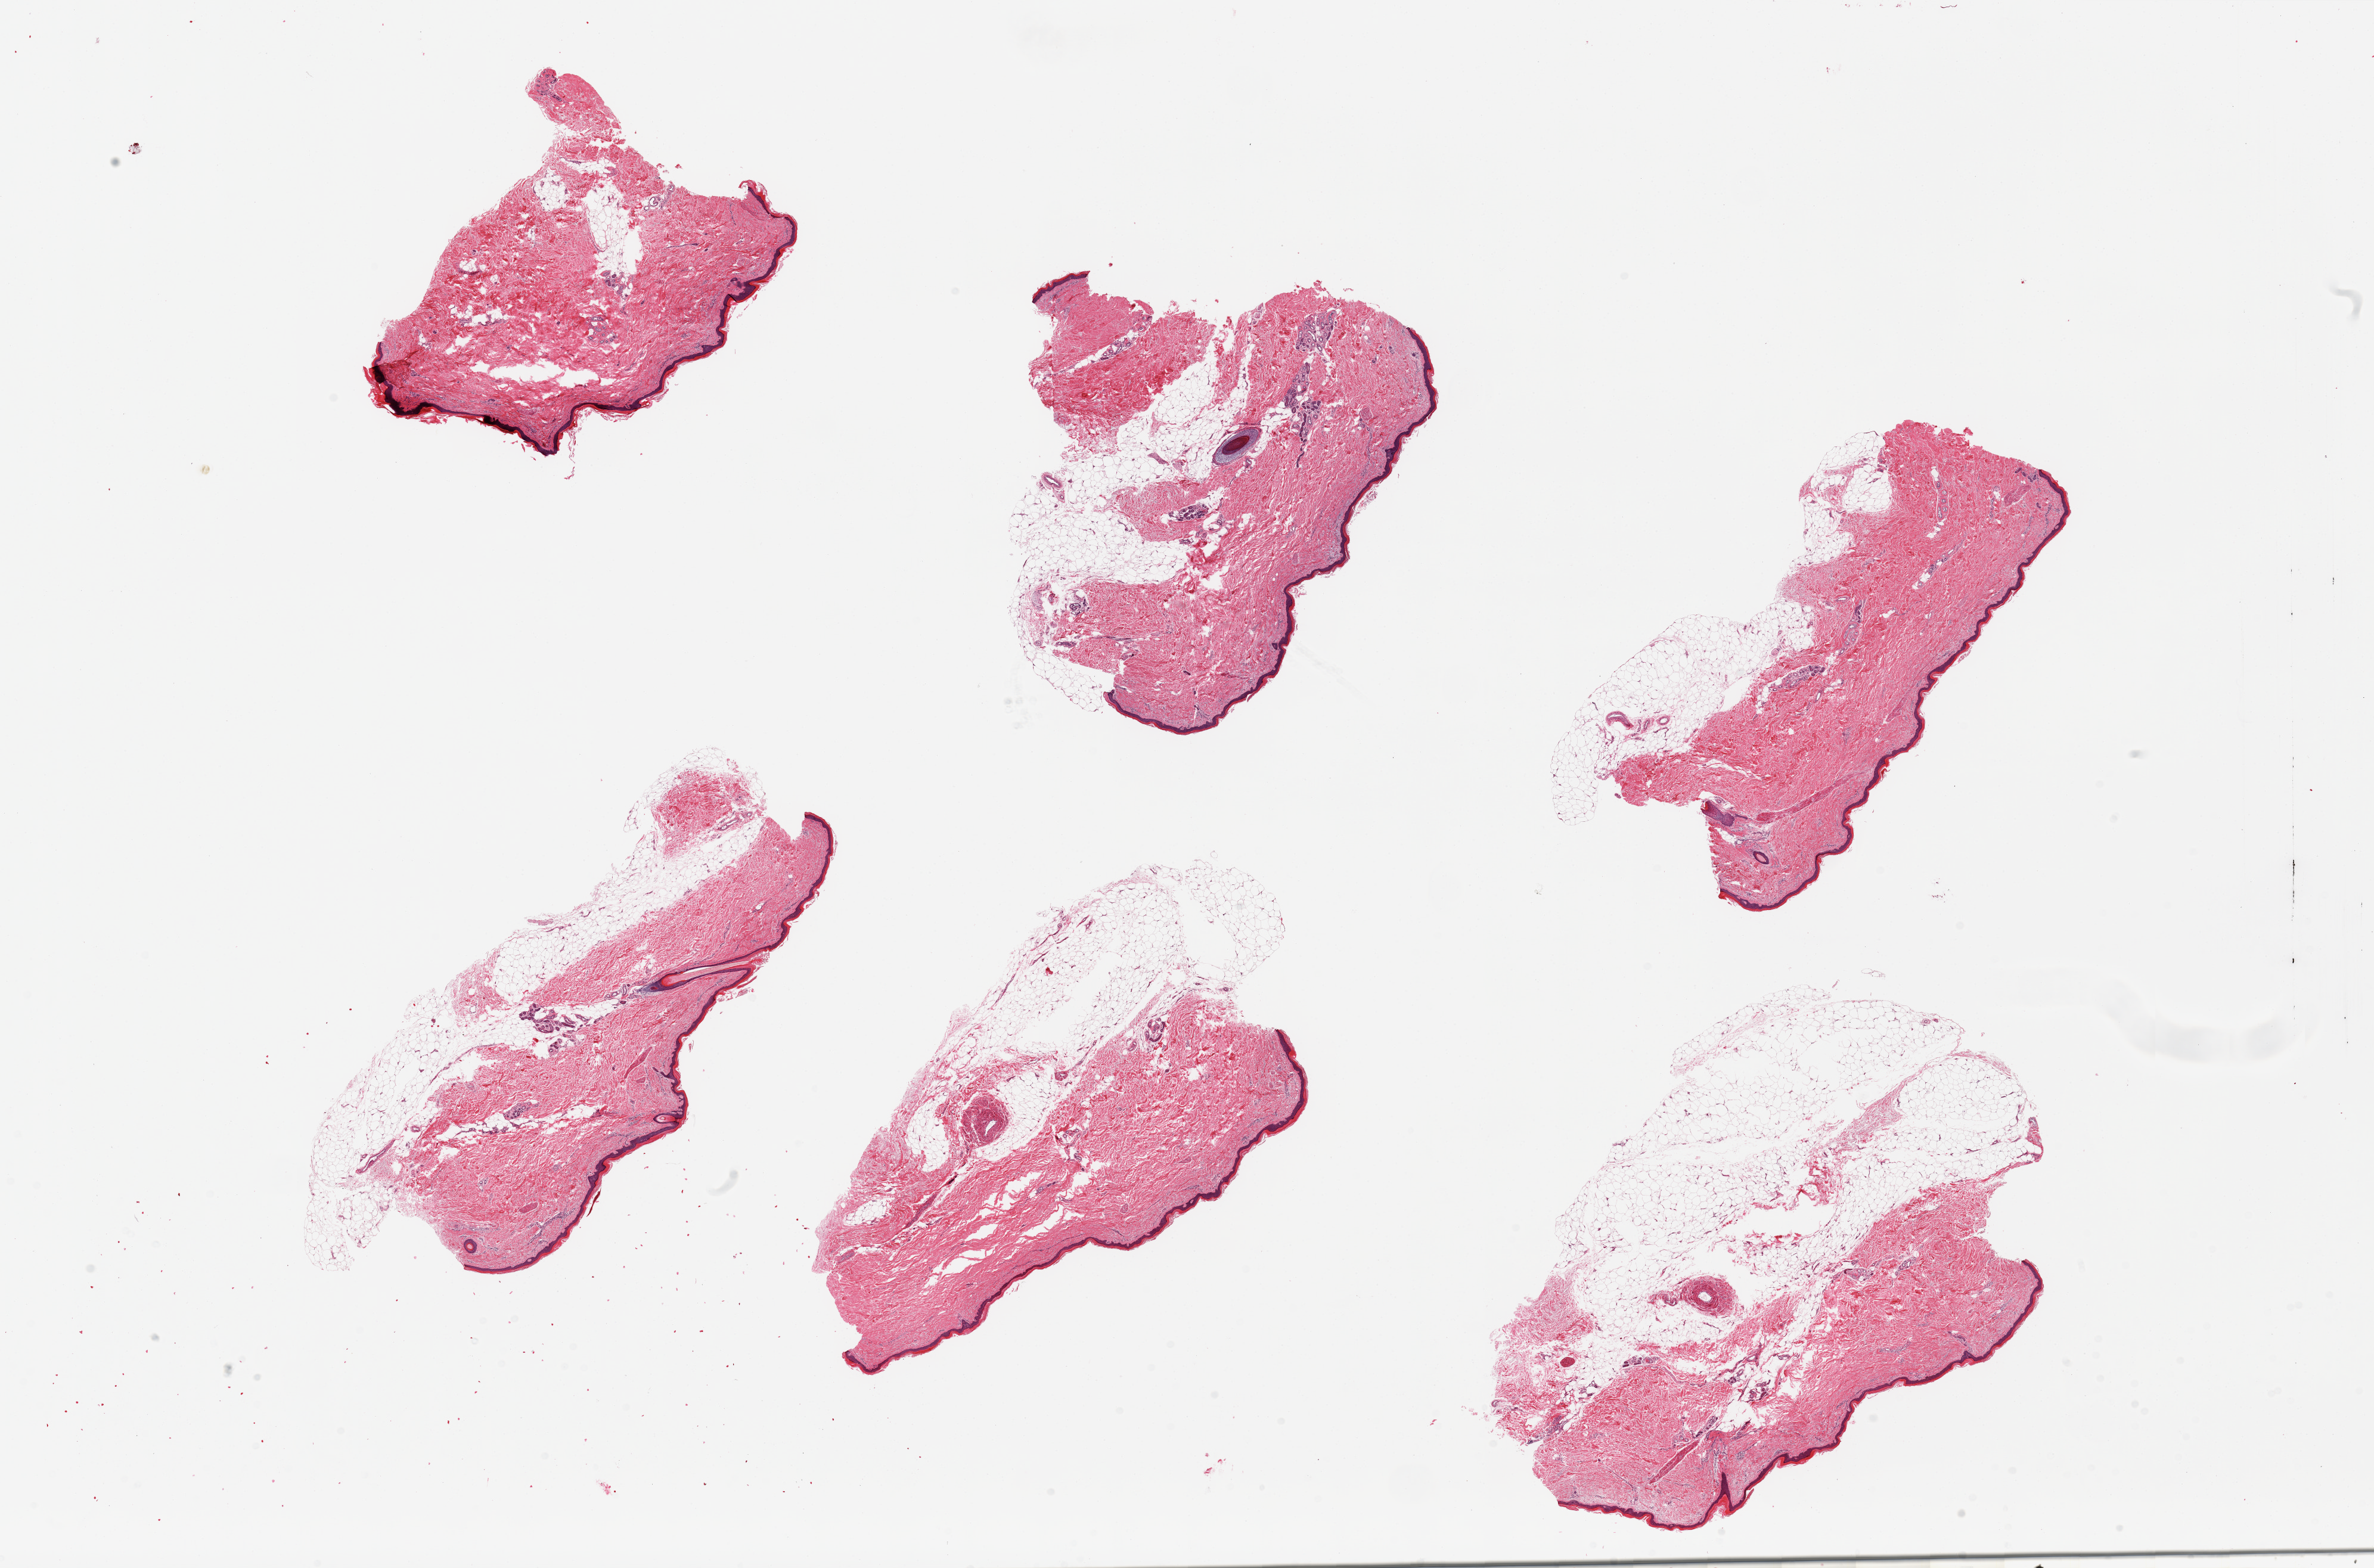
Haematoxylin and eosin whole-slide image — whole scanned area (about 31.5 x 20.8 mm, from a 20x scan) shown as a low-resolution overview; PAXgene-fixed paraffin-embedded (PFPE) section; target tissue: skin of lower leg; tissue donor sample. Donor: male.
Reviewer comment on this tissue sample: 6 pieces, adherent fat up to 3mm thick, squamous epithelium is ~50-60 microns.